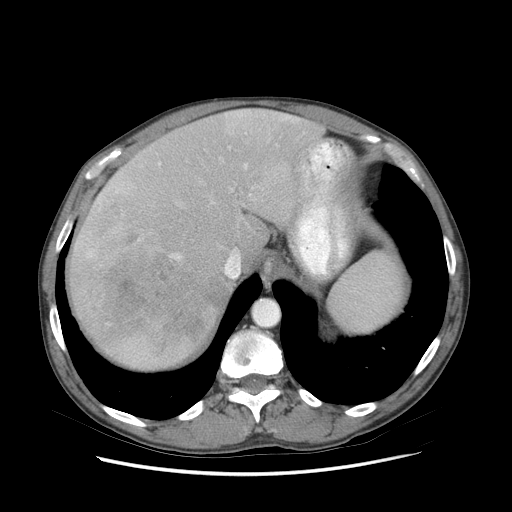
Contrast-enhanced abdominal CT (liver protocol), one axial slice. Position 62 of 89 along the scan axis. Reconstruction kernel STANDARD. 140 kVp. Soft-tissue window (W 400 / L 40 HU). 2.5 mm slice thickness. 512 × 512 image matrix. Case-level facts recorded for this patient, not image findings: diagnosis: hepatocellular carcinoma (patient treated with transarterial chemoembolisation; whether this scan precedes or follows treatment is not stated here); TNM stage (as recorded): Stage-IIIB; Child-Pugh class: A; tumour differentiation: moderately differentiated; tumour nodularity: multinodular.
Outlined on this slice (semi-automatic segmentation, software-assisted and operator-edited):
- liver parenchyma outside the tumour (the mass and vessels are separate outlines, so this box may not span the whole liver): bounding box [x1, y1, x2, y2] px = [68, 108, 346, 368]
- mass: [76, 202, 220, 347]
- liver vessels: [87, 112, 340, 259]